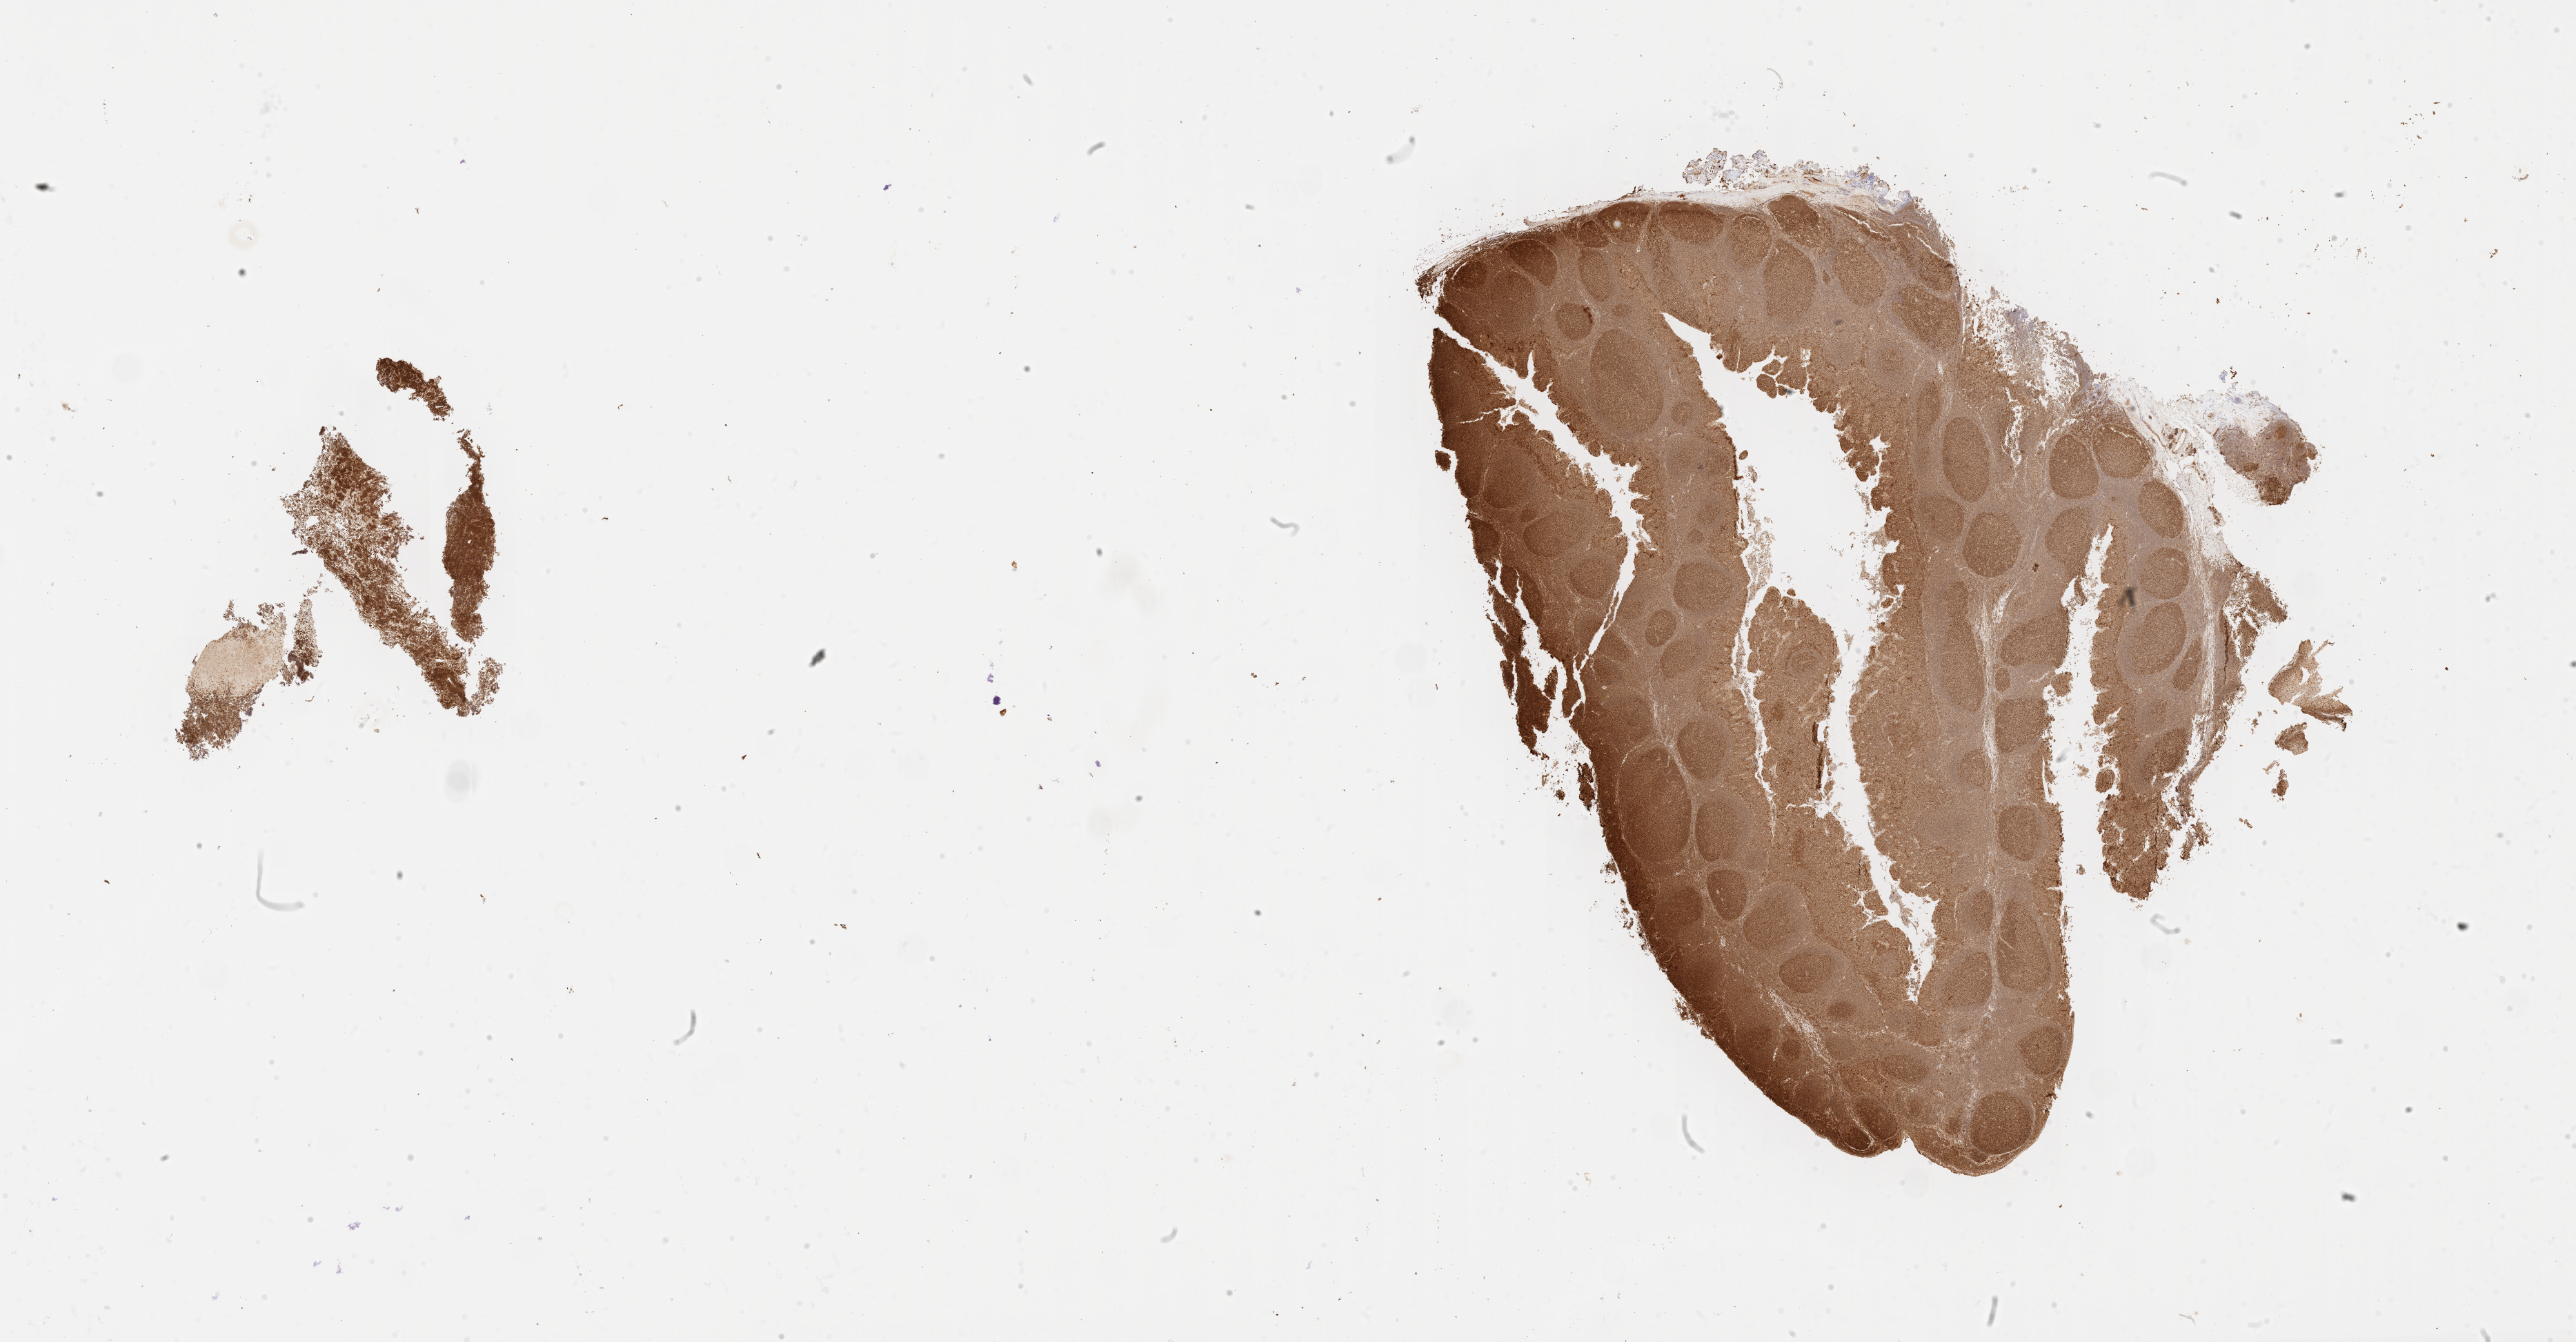
Whole-slide image, immunohistochemical stain for BCL6, low-resolution overview of the scanned area, about 30.2 x 15.7 mm; tumor tissue; site: pelvis. Female patient; age at initial diagnosis 7 years.
Histologic diagnosis: Burkitt lymphoma, NOS.